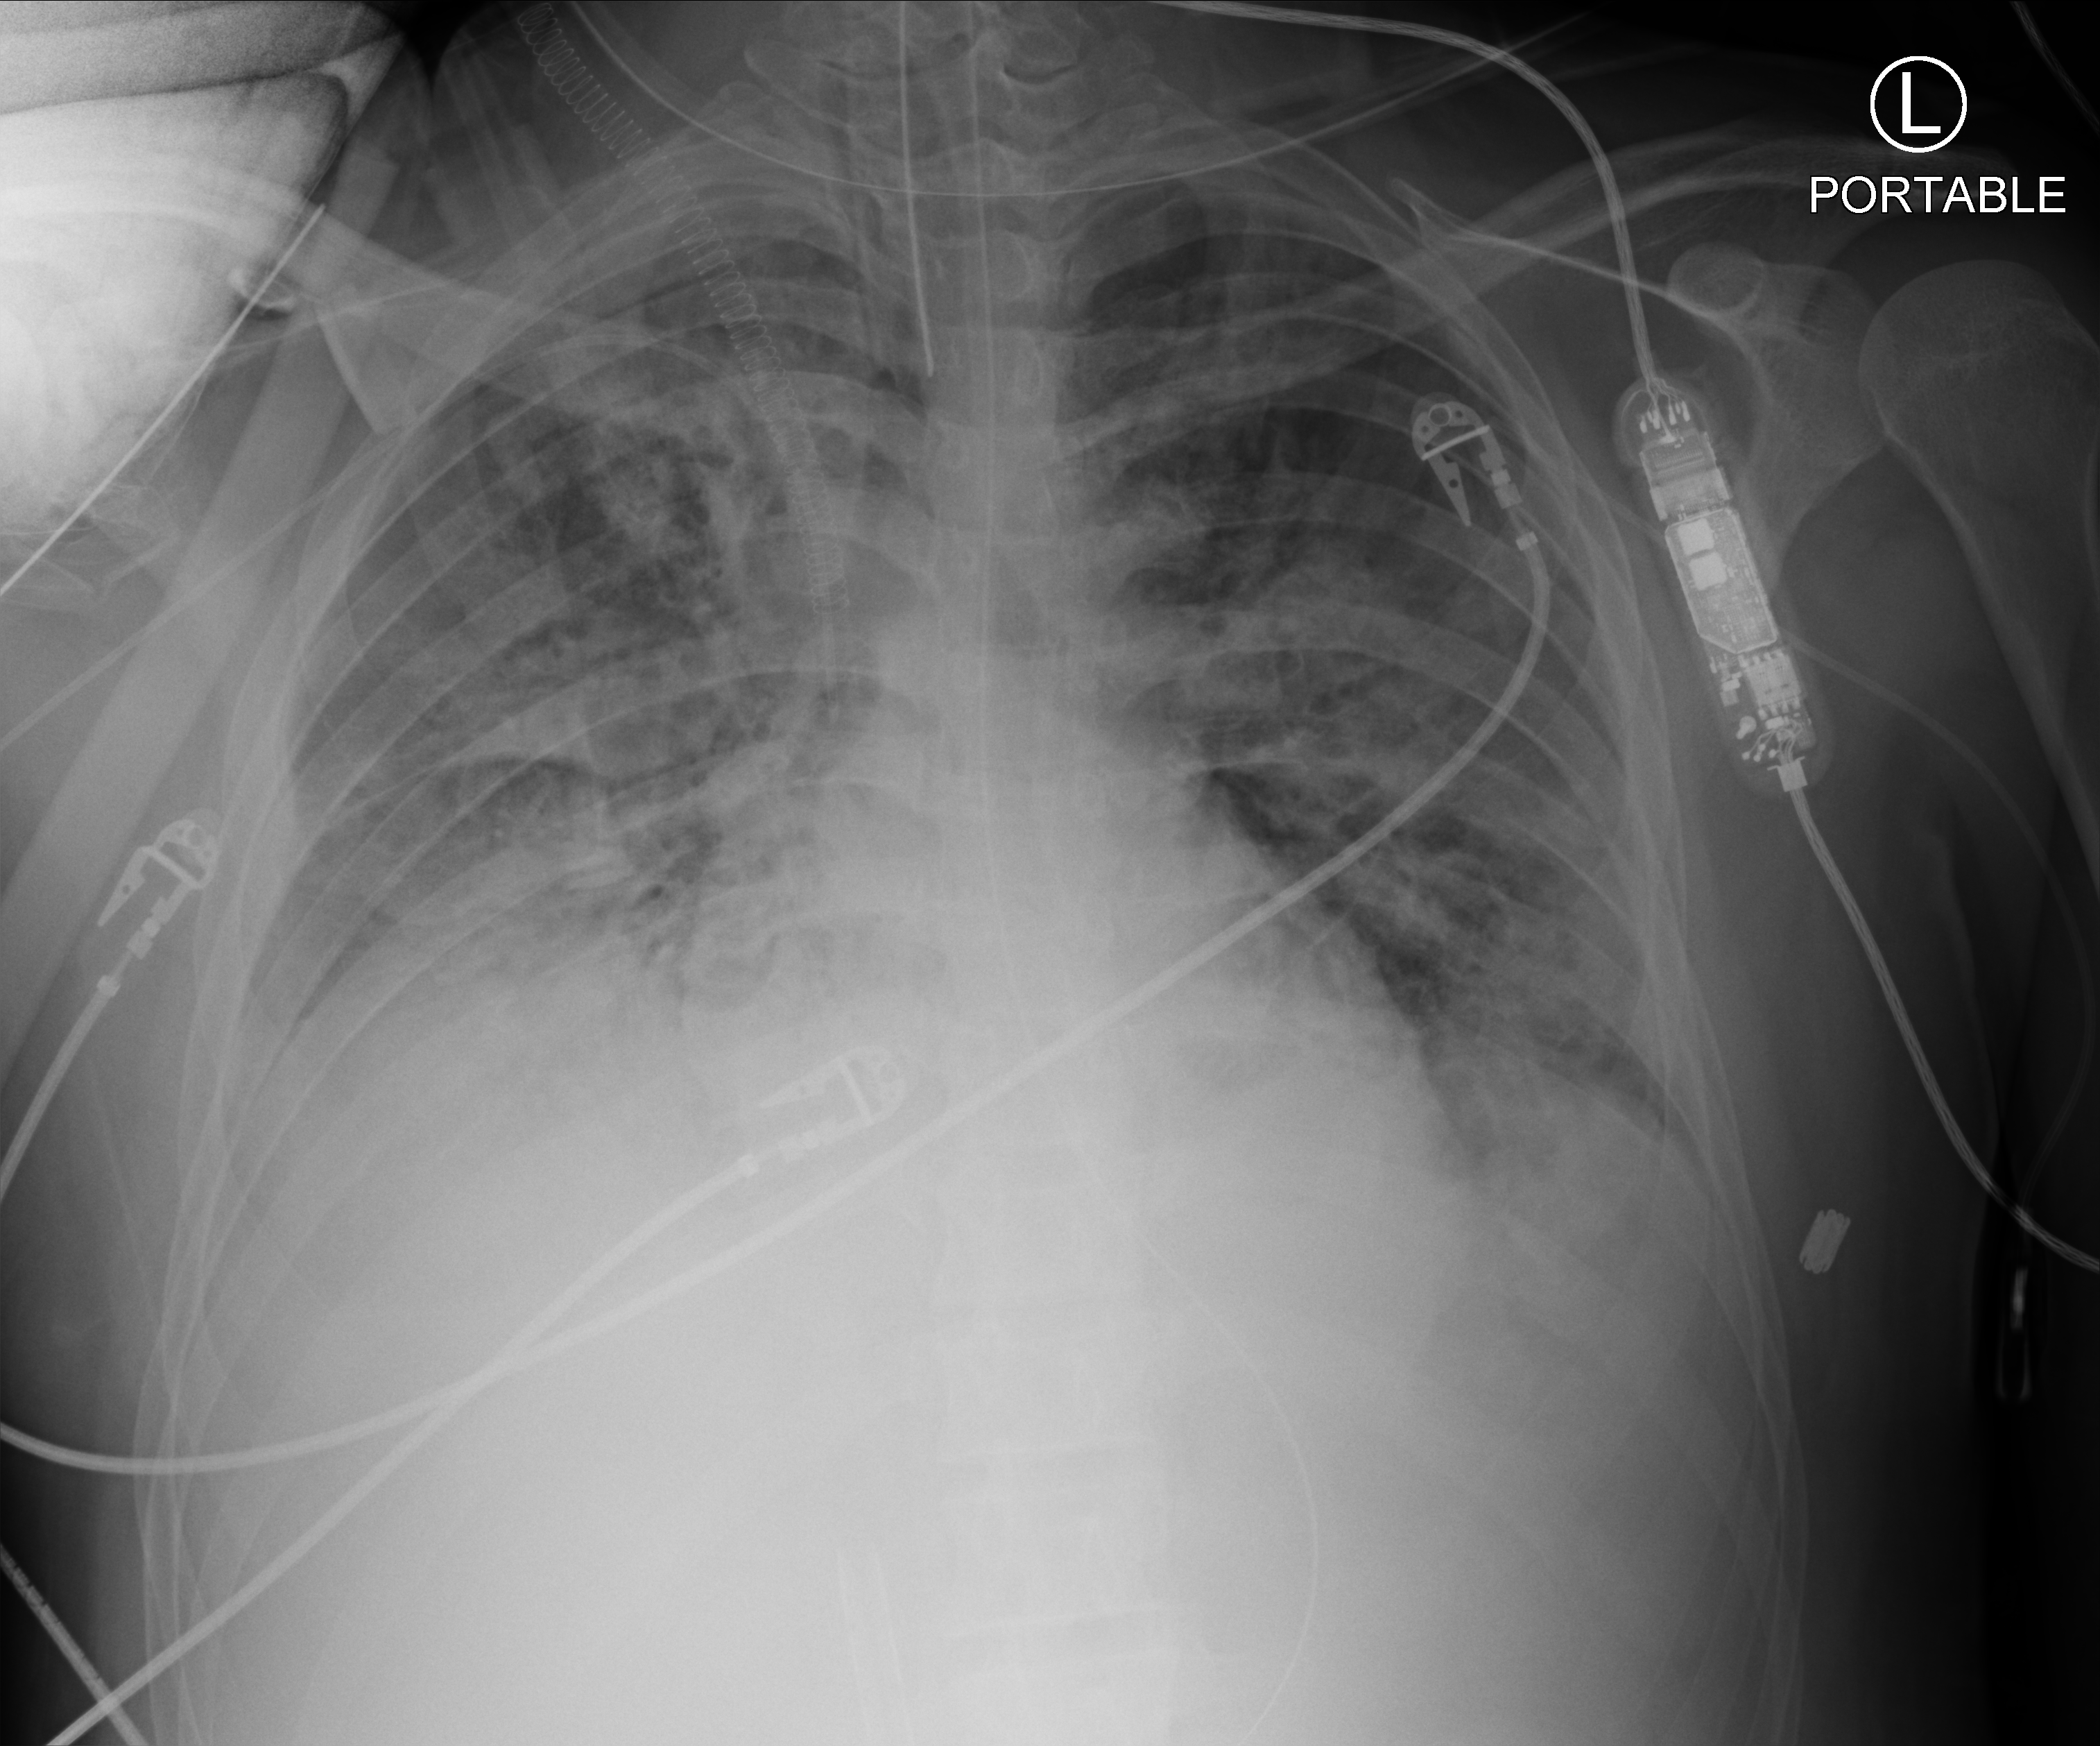
Chest X-ray (portable), anteroposterior (AP) projection. Patient hospitalised with COVID-19, aged 18–59 years.
From the hospital-stay record, not from the radiograph (when in the stay this image was taken is not recorded): diabetes (admission record): no.